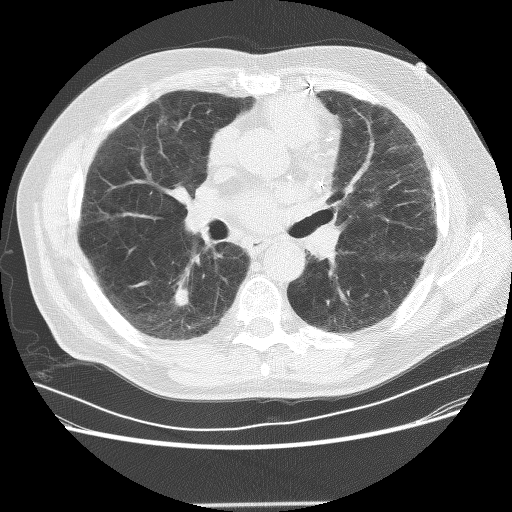
Chest CT (low-dose screening protocol), one axial image; baseline screening round; lung window (W 1500 / L -600 HU); lung (sharp) reconstruction kernel (BONE); slice 125 of 281 in the series. Male, age 72 years at enrolment. Former smoker at enrolment.
Expert-annotated lung lesion, bounding box <151,275,202,322> (left, top, right, bottom; pixels). The screening reader recorded 2 non-calcified nodules or masses ≥4 mm on this exam (right lower lobe, left lower lobe); which of them this box marks is not recorded. Official screen result: positive, change unspecified: nodule(s) >= 4 mm or enlarging nodule(s), mass(es), or other non-specific abnormalities suspicious for lung cancer. Lung cancer was diagnosed 436 days after this screen: squamous cell carcinoma, NOS, right lower lobe, poorly differentiated (G3), stage IB (AJCC 6th edition), 42 mm at pathology.